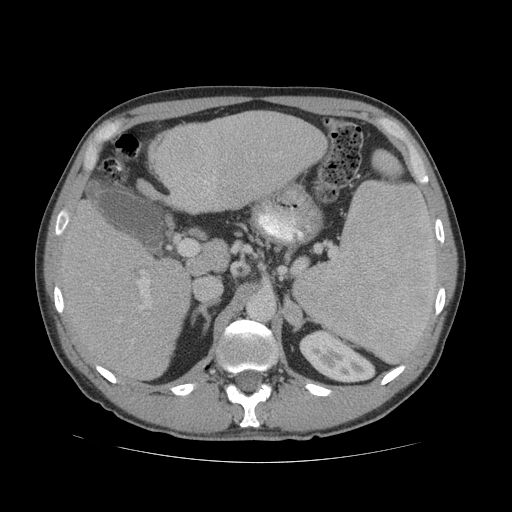
Contrast-enhanced abdominal CT (liver protocol), one axial slice. 140 kVp. Soft-tissue window (W 400 / L 40 HU). 2.5 mm slice thickness. 512 × 512 image matrix, field of view 400 × 400 mm. Case-level facts recorded for this patient, not image findings: diagnosis: hepatocellular carcinoma (patient treated with transarterial chemoembolisation; whether this scan precedes or follows treatment is not stated here); TNM stage (as recorded): Stage-IVB.
Outlined on this slice (semi-automatically segmented with operator editing):
- liver parenchyma outside the tumour (the mass and vessels are separate outlines, so this box may not span the whole liver): box from (x=56, y=110) to (x=326, y=380) px
- liver vessels: (x=59, y=140)–(x=216, y=308)